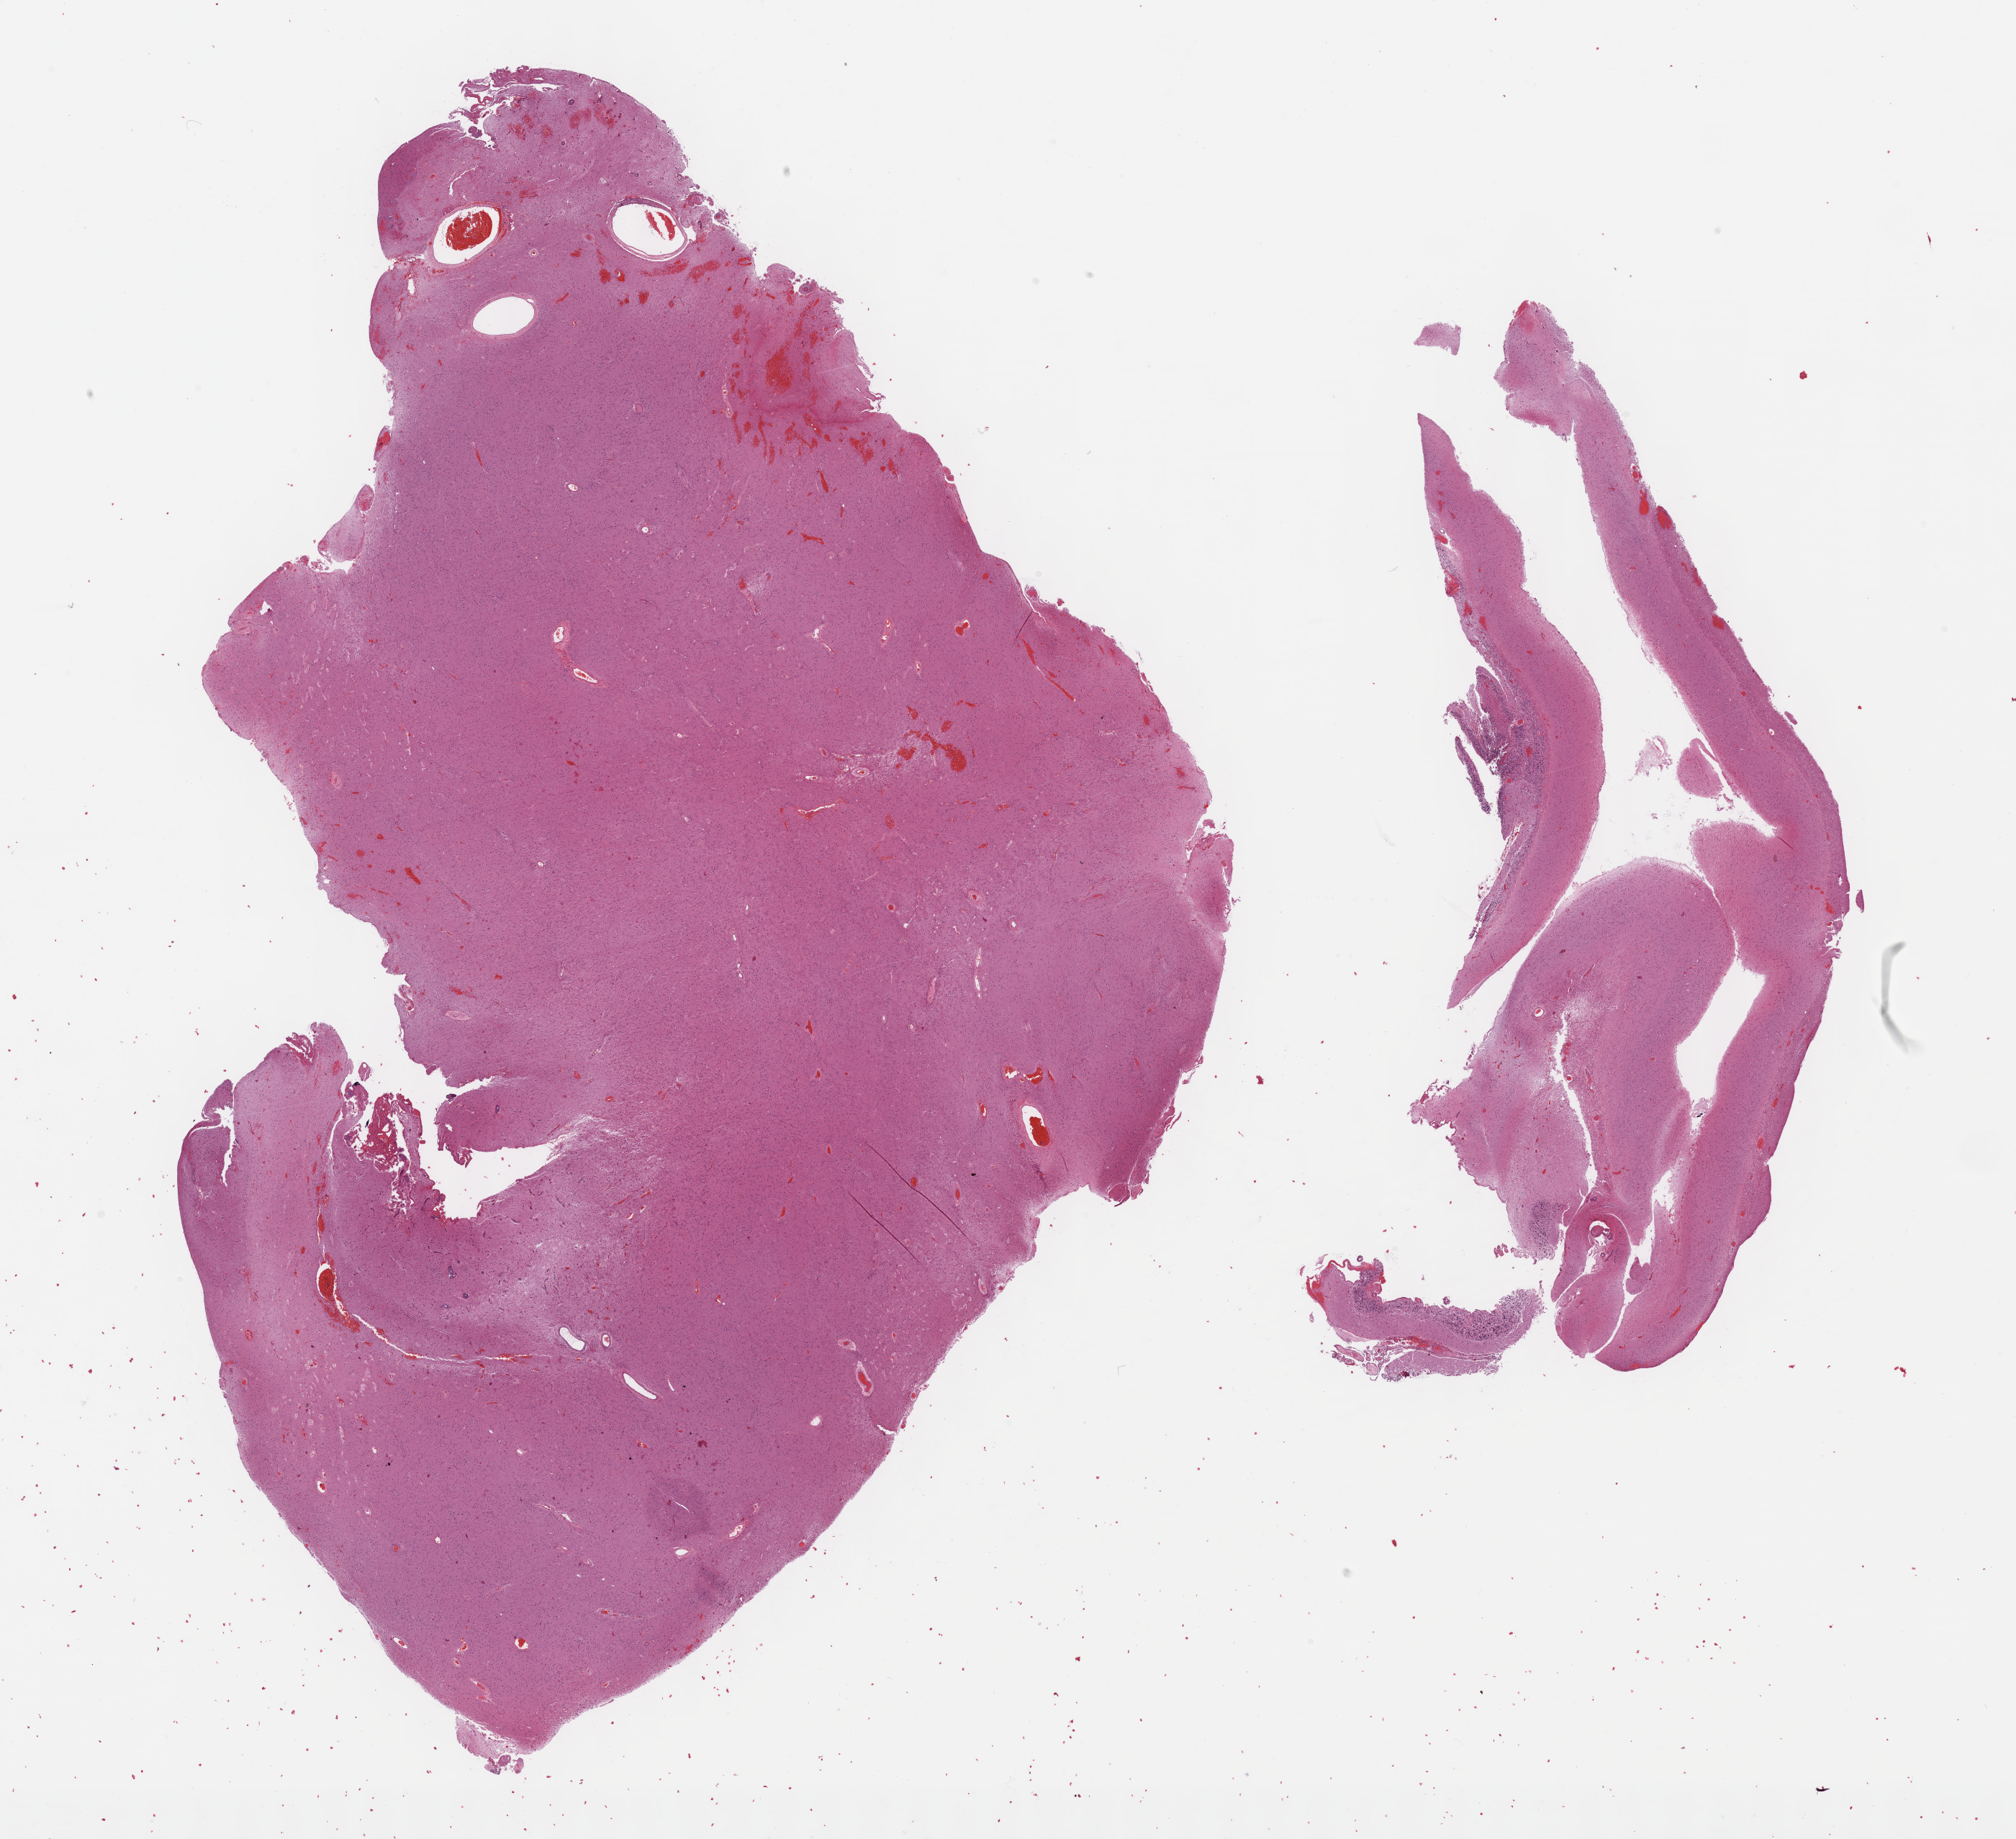
Hematoxylin and eosin (H&E) stained whole-slide image, a low-resolution overview of the entire scanned area, about 22.7 x 20.7 mm (from a 40x scan); FFPE section; primary tumour sample from the brain. Patient: female, age at initial diagnosis 32 years. Histologic grade: G2 (moderately differentiated).
Laterality: midline. Diagnosis: Astrocytoma, NOS.